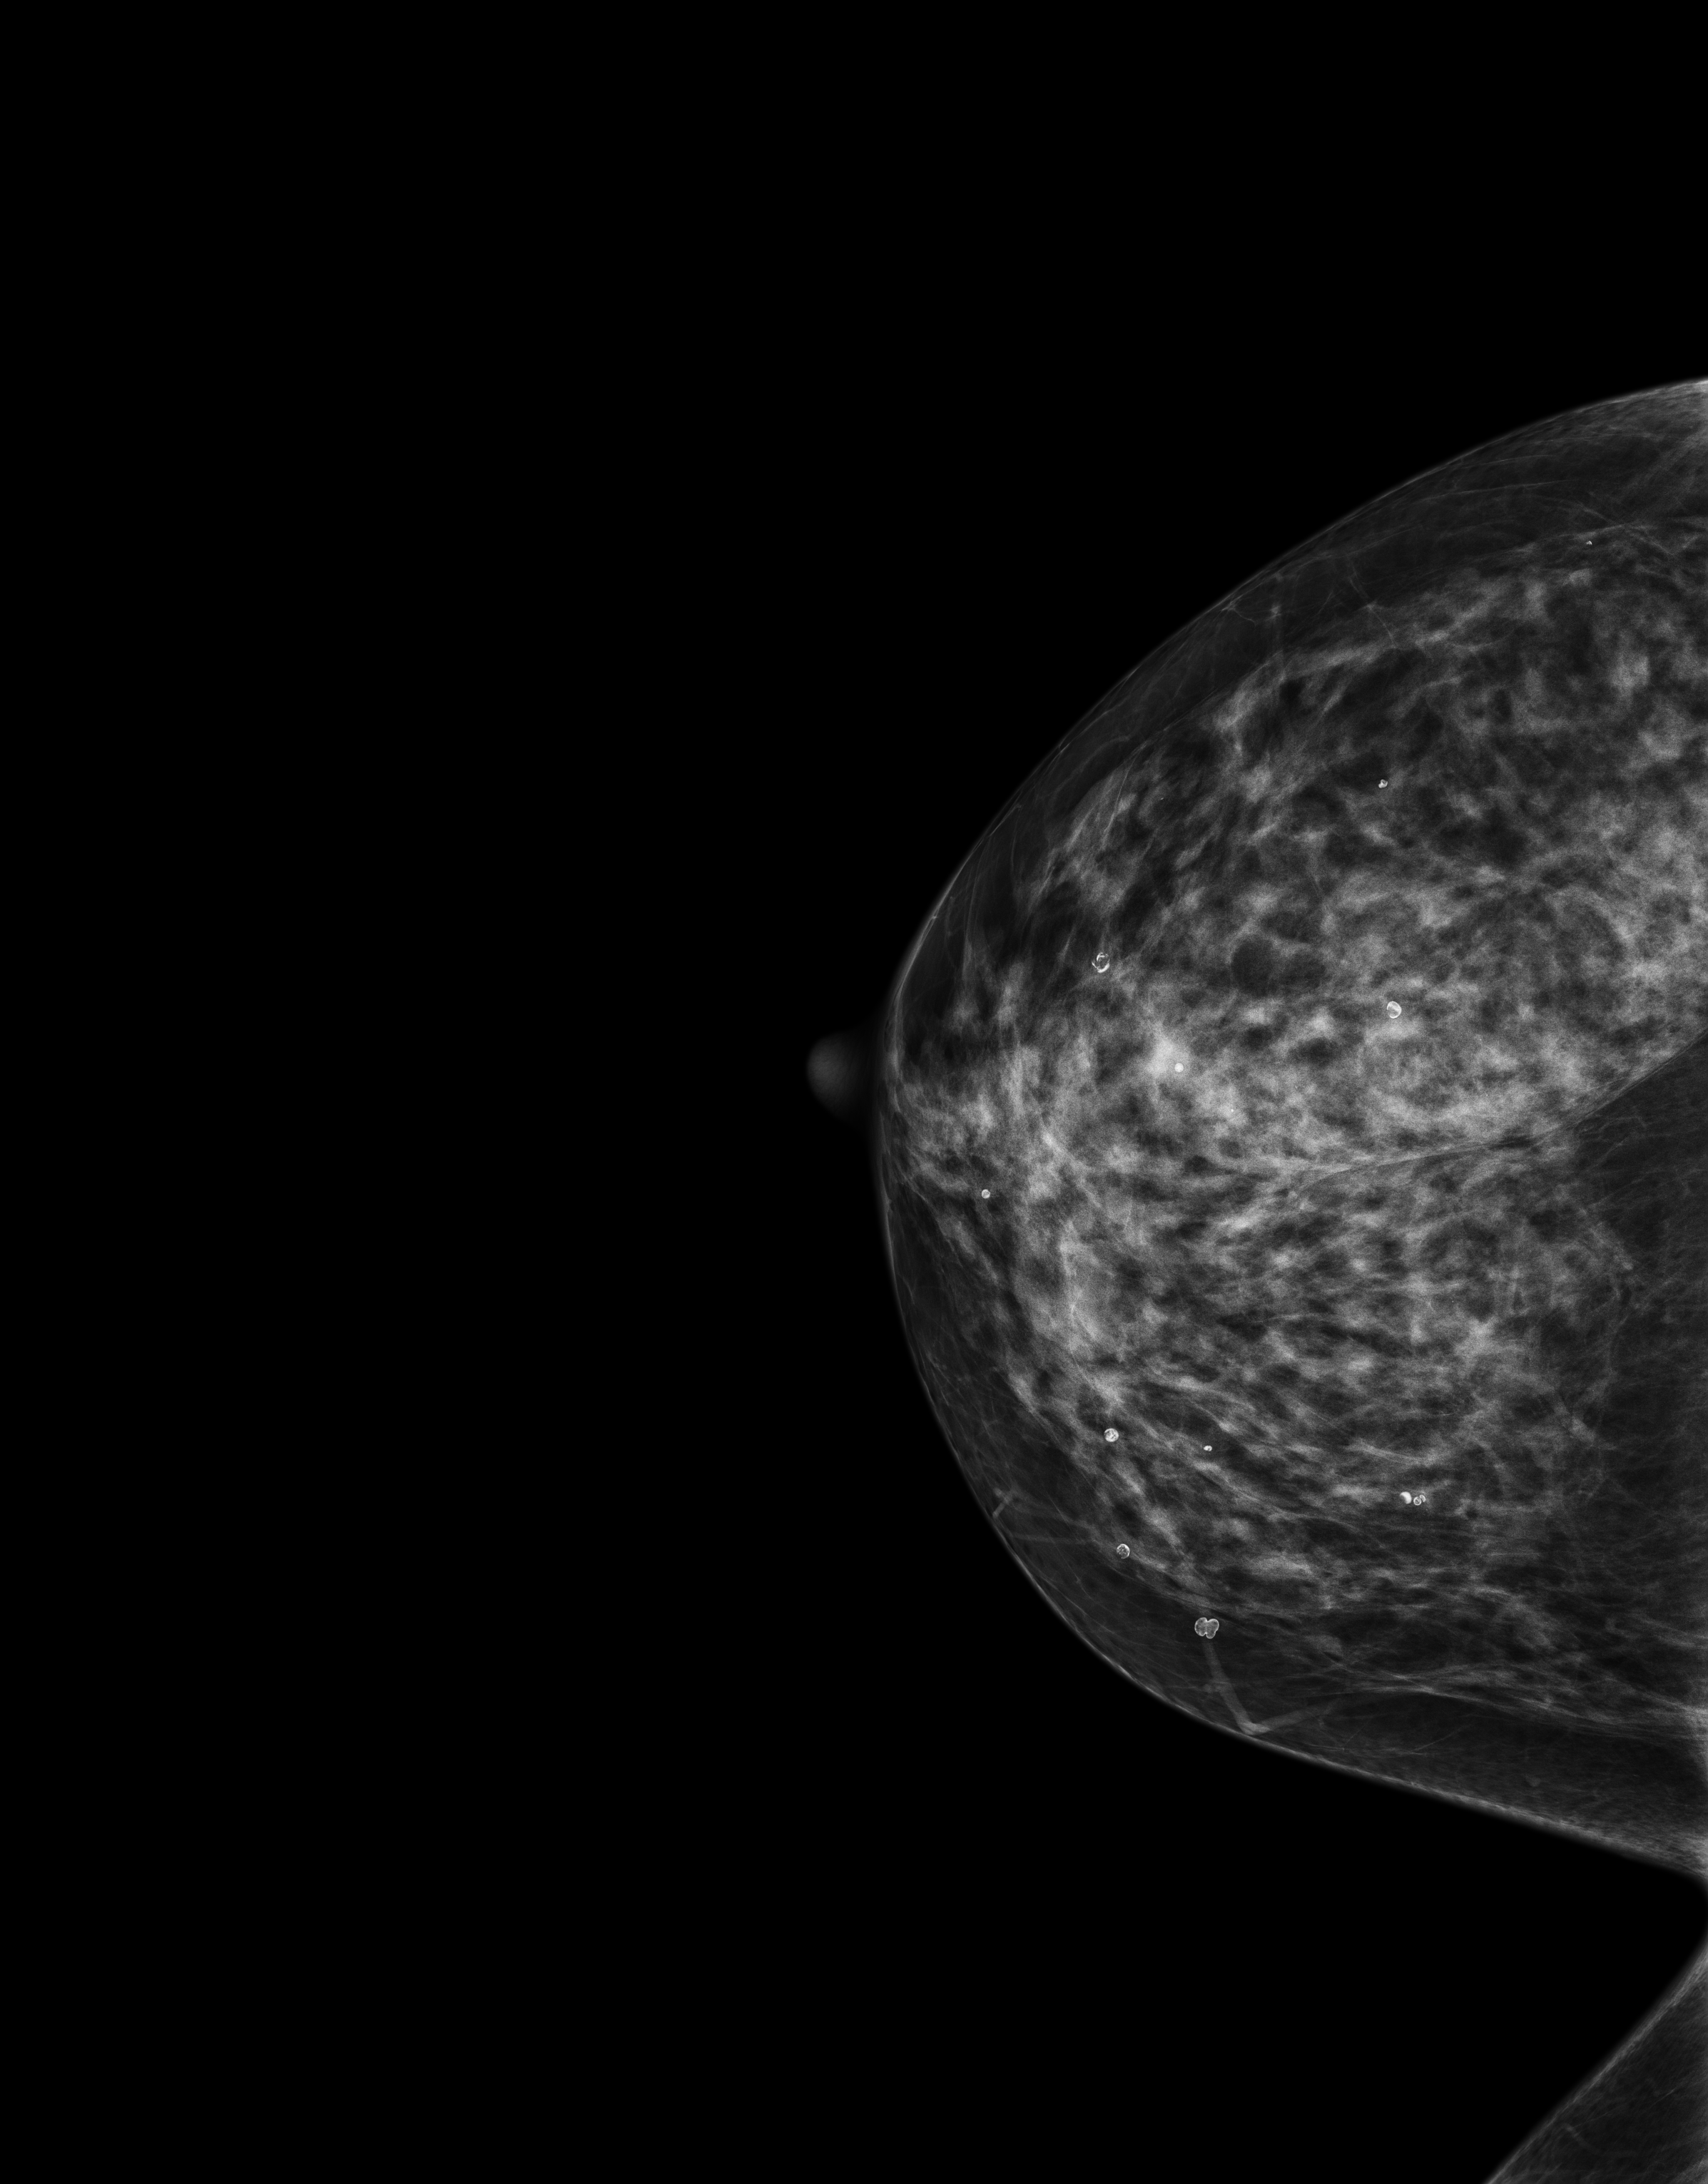
Digital mammogram (FFDM); right breast; craniocaudal (CC) view; annual screening mammography examination. Patient: female, 66 years.
BI-RADS breast density category at the screening exam (both breasts, scale 1–4): 3. Final BI-RADS assessment for this screening round (tomosynthesis exam, both breasts): category 1. Recall: no recall after this screen.